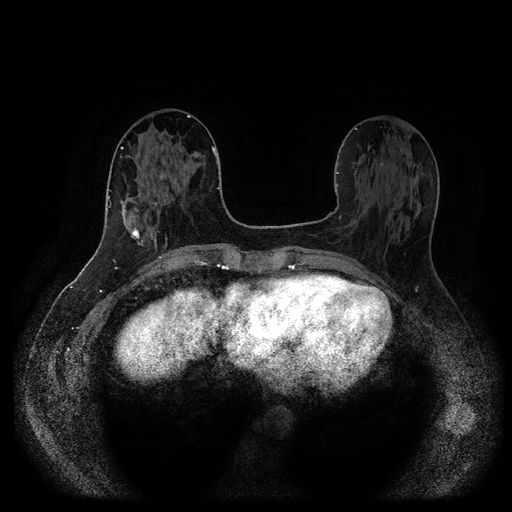
Breast MRI (dynamic contrast-enhanced, multi-phase), one axial slice; slice 42 of 116 in the series (ordered by position); dynamic contrast-enhanced series, time point 2 of 5 at this slice position (early post-contrast); 1.5 T; TE 2.6 ms, TR 5.3 ms; 512 × 512 image matrix, field of view 360 × 360 mm. Patient: female, 58 years.
Outlined on this slice (semi-automatic segmentation, software-assisted and operator-edited):
- breast lesion (labelled 'tumour' in the annotation; benign lesions carry a separate 'benign' label): bounding box [x1, y1, x2, y2] px = [129, 225, 140, 242]